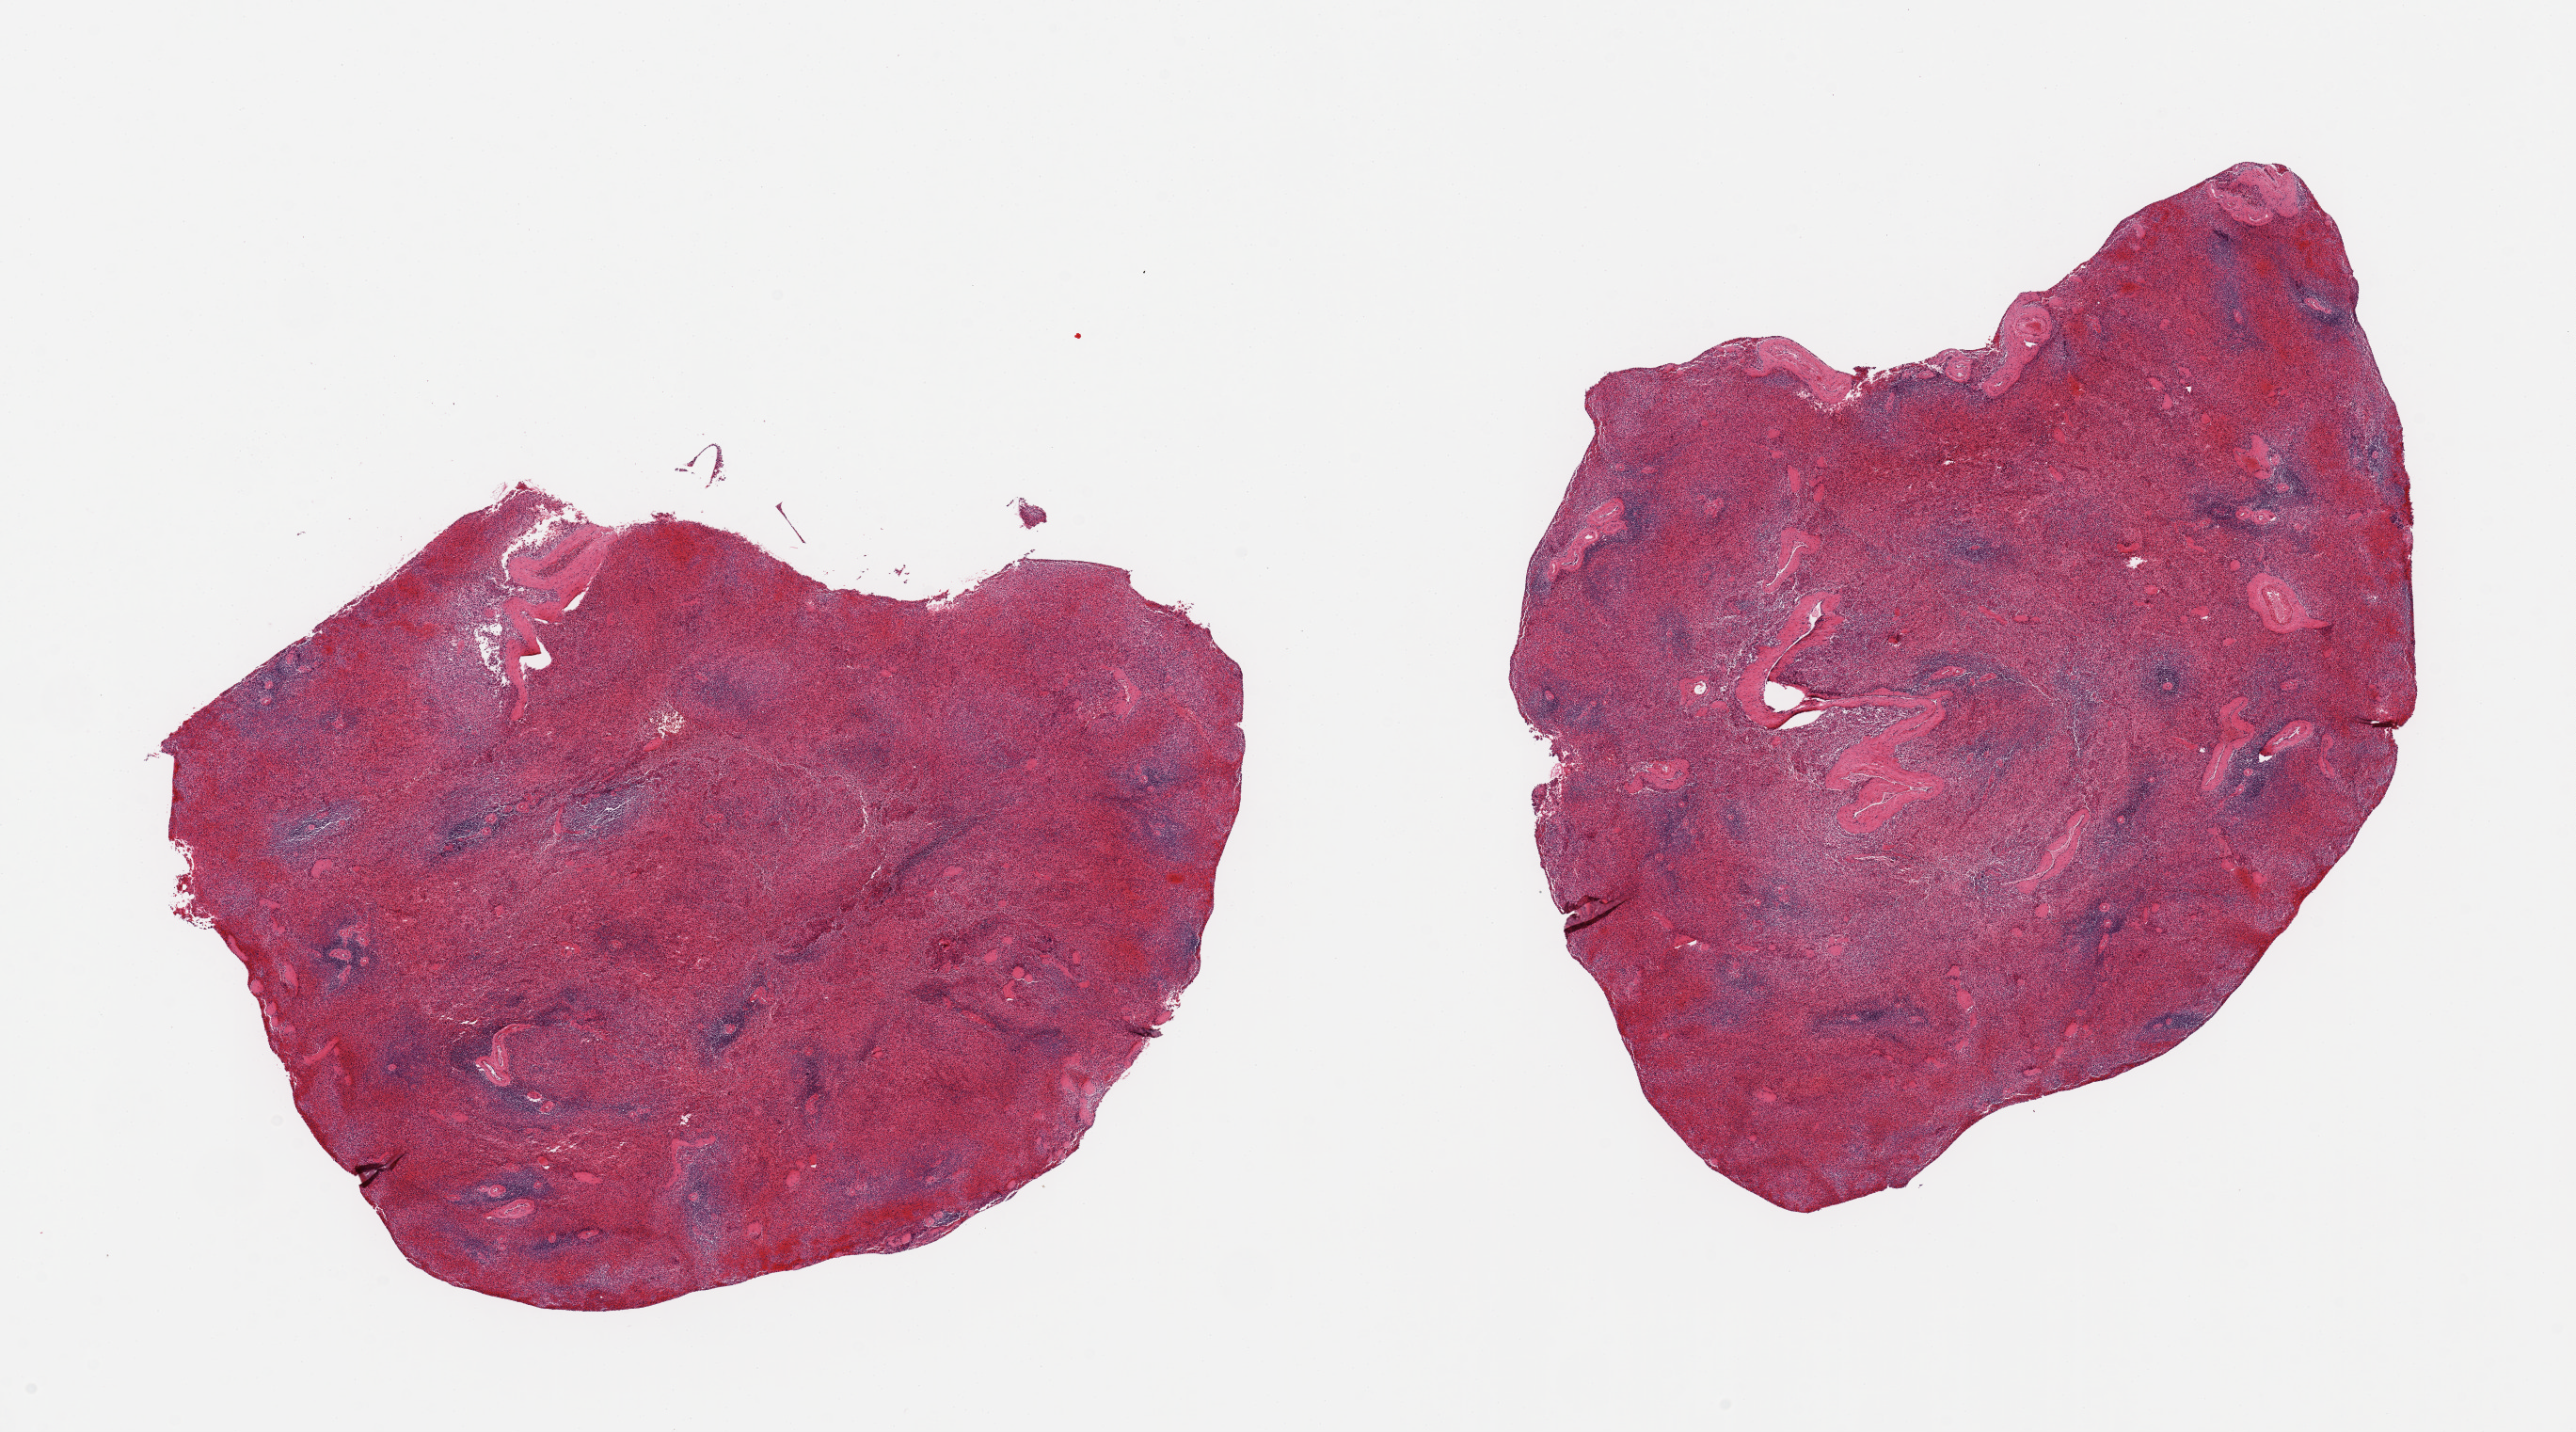
Hematoxylin and eosin (H&E) whole-slide image, low-resolution overview of the scanned area, about 21.7 x 12.0 mm. PAXgene-fixed, paraffin-embedded tissue. Target tissue: spleen. Donor tissue sample. Donor sex: female.
Review note (as recorded): 2 pieces, marked congestion.